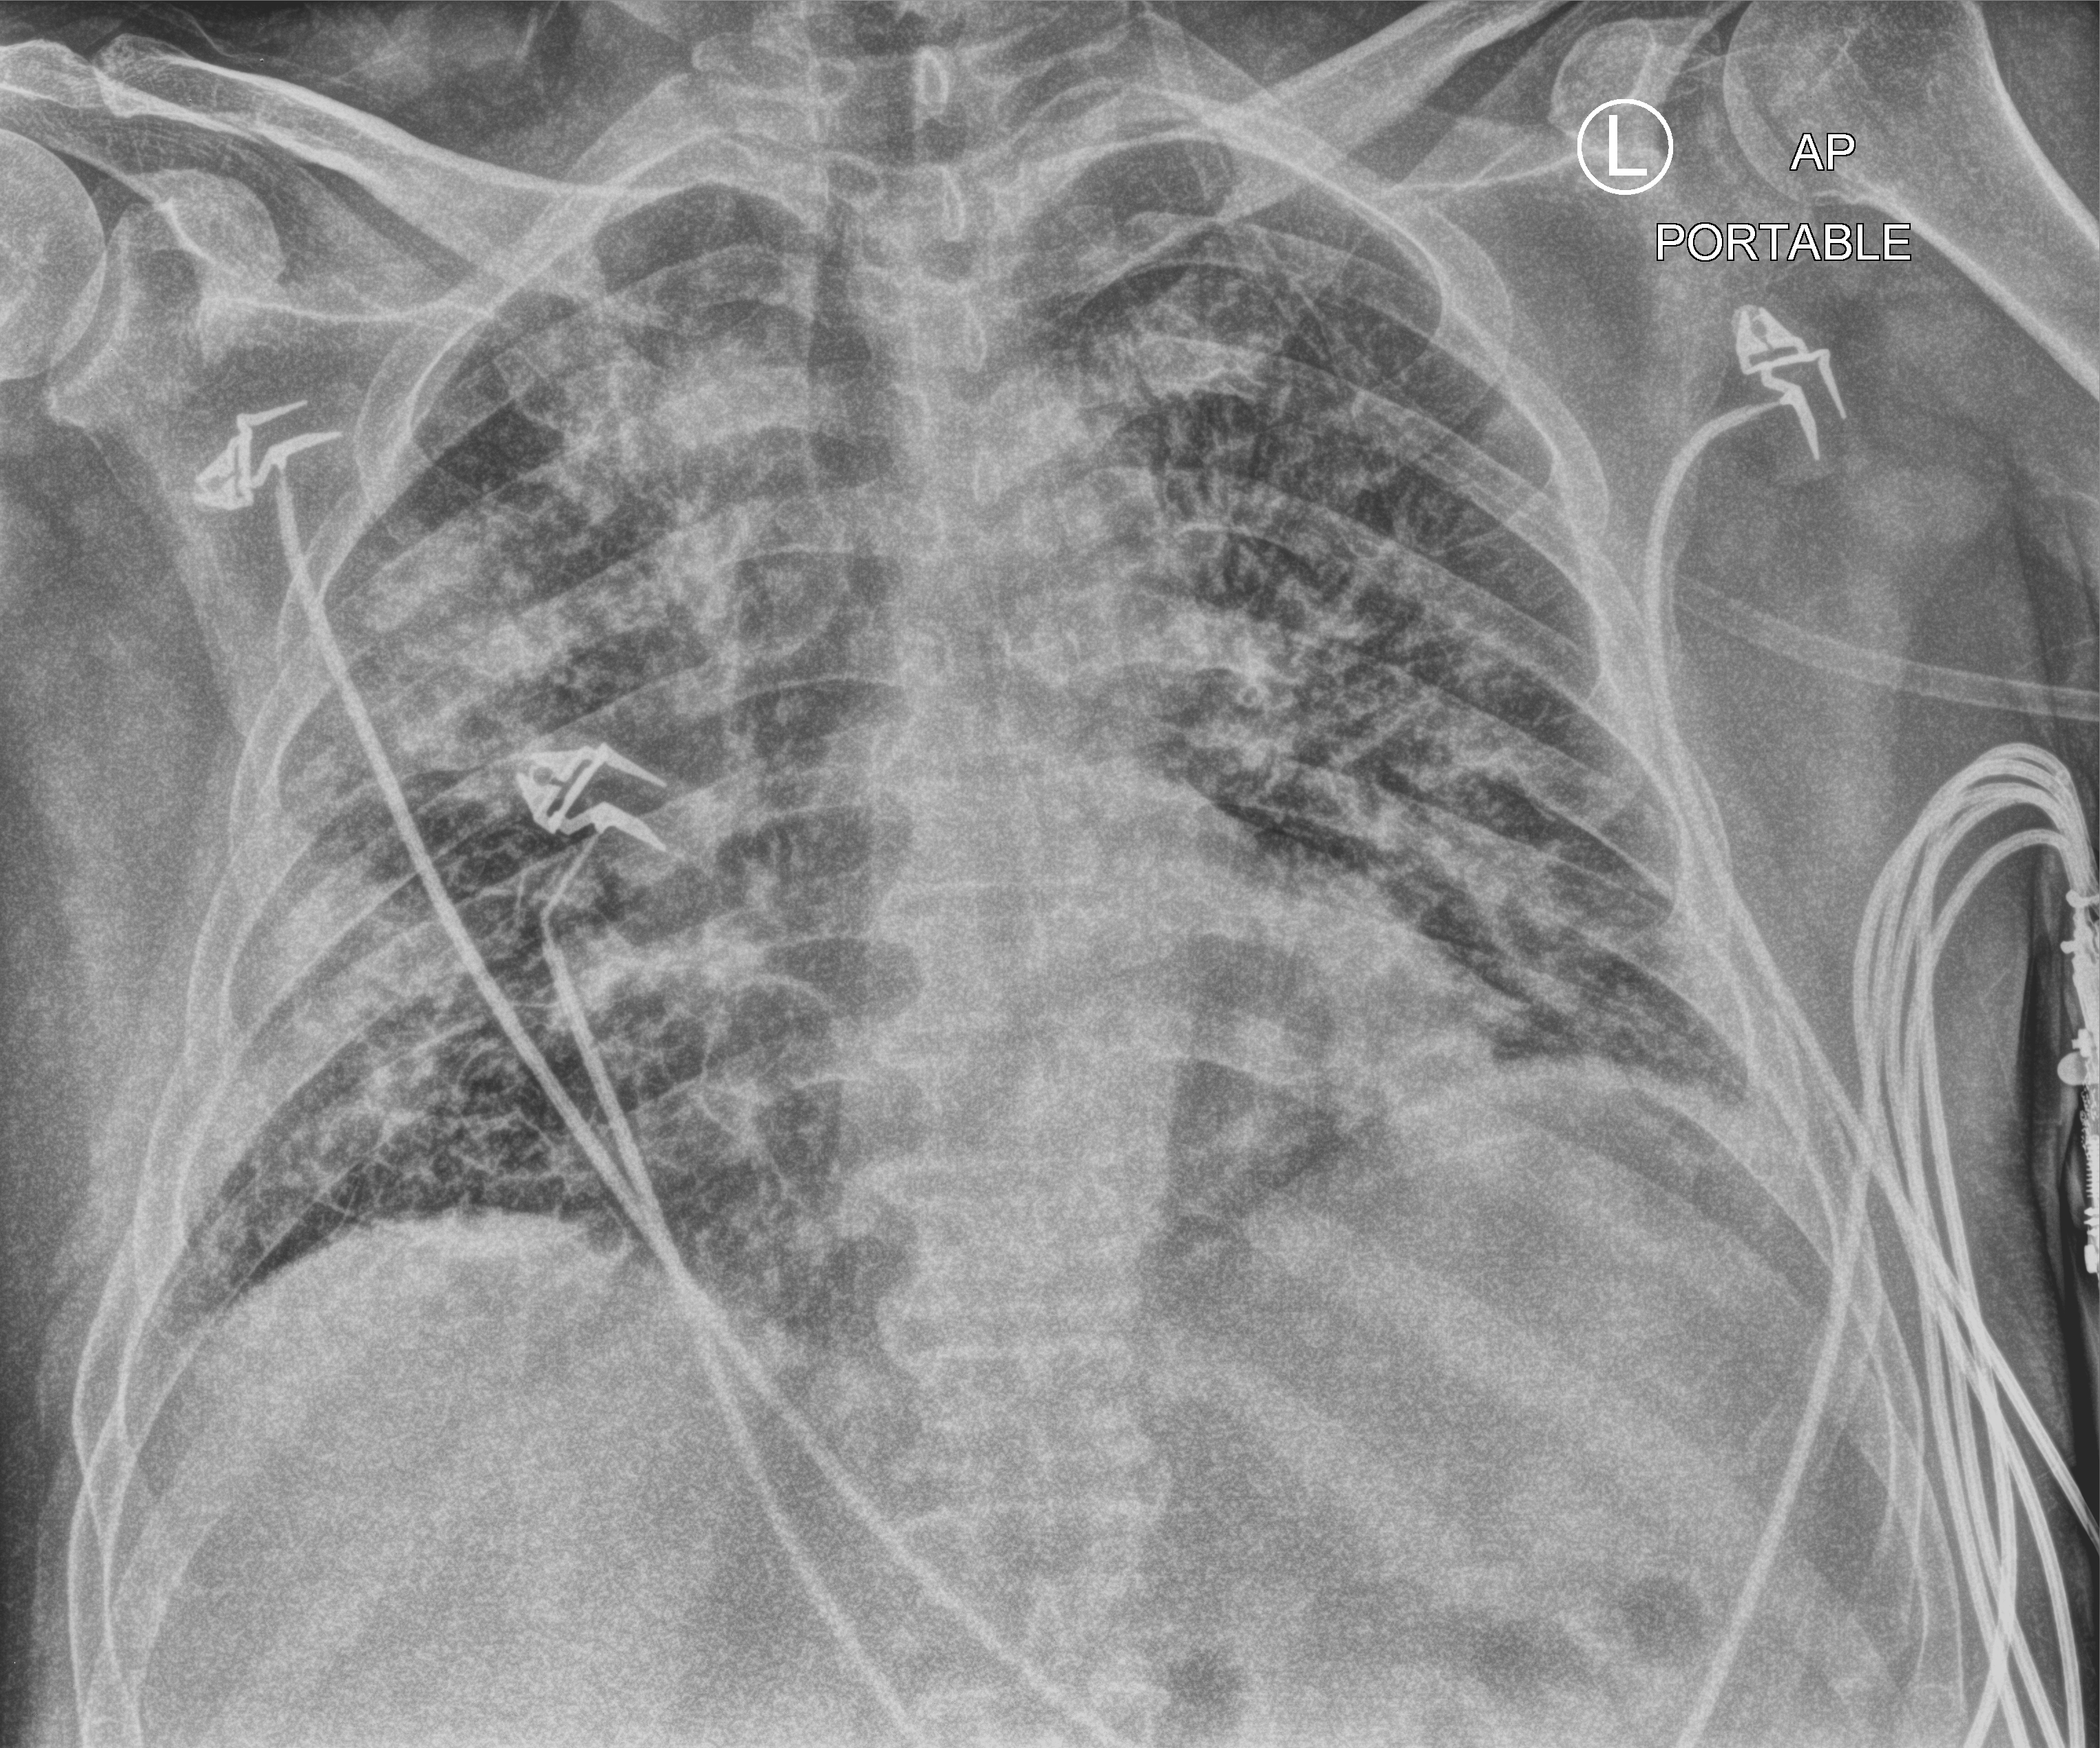
Bedside chest radiograph (computed radiography), anteroposterior (AP) projection. Male patient hospitalised with COVID-19, age 60–74 years.
From the hospital-stay record, not from the radiograph (when in the stay this image was taken is not recorded): admitted to intensive care during this hospital stay: no.